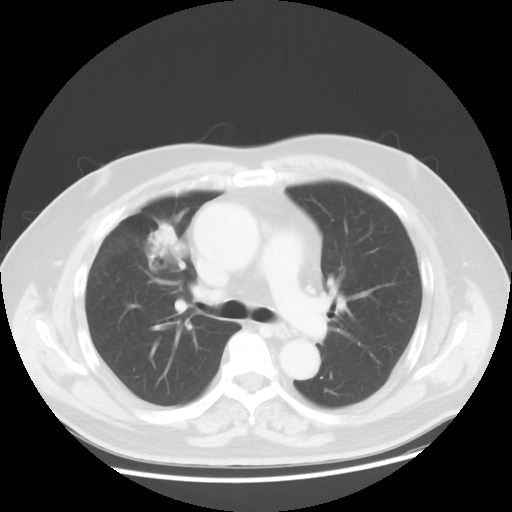
Chest CT, one axial slice. Position 28 of 48 along the scan axis. Reconstruction kernel STANDARD. 120 kVp. Lung window (W 1500 / L -600 HU). 512 × 512 image matrix. Patient: male, 60 years. Case-level facts recorded for this patient, not image findings: clinical TNM (as recorded): T2 N3 M0; histopathological grade: G2-3.
Outlined on this slice (rectangle marked by the reading radiologist):
- lung tumour (recorded histology: adenocarcinoma): bounding box <134,215,186,280> (left, top, right, bottom; pixels)